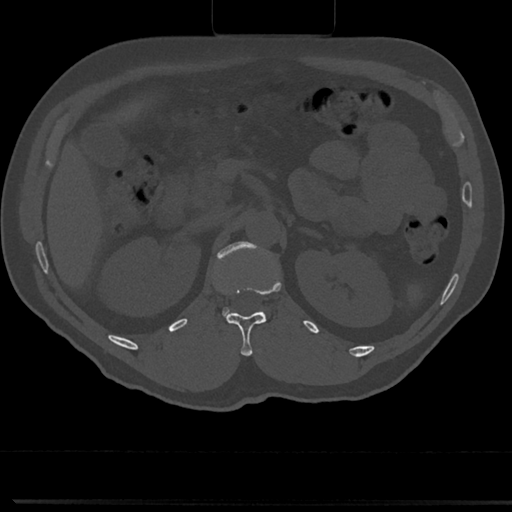
CT including the spine, one axial slice; slice 120 of 817 in the series (ordered by position); reconstruction kernel Br40s/3; bone window (W 1800 / L 400 HU); 0.5 mm slice thickness; 512 × 512 image matrix, field of view 355 × 355 mm. Patient: male, 61 years. From the clinical record (not read from this slice): primary cancer: prostate.
Outlined on this slice (semi-automatically segmented with operator editing):
- L1 vertebra: bounding box (x1, y1, x2, y2) in pixels: (212, 241, 276, 322)
- T12 vertebra: (224, 311, 267, 355)